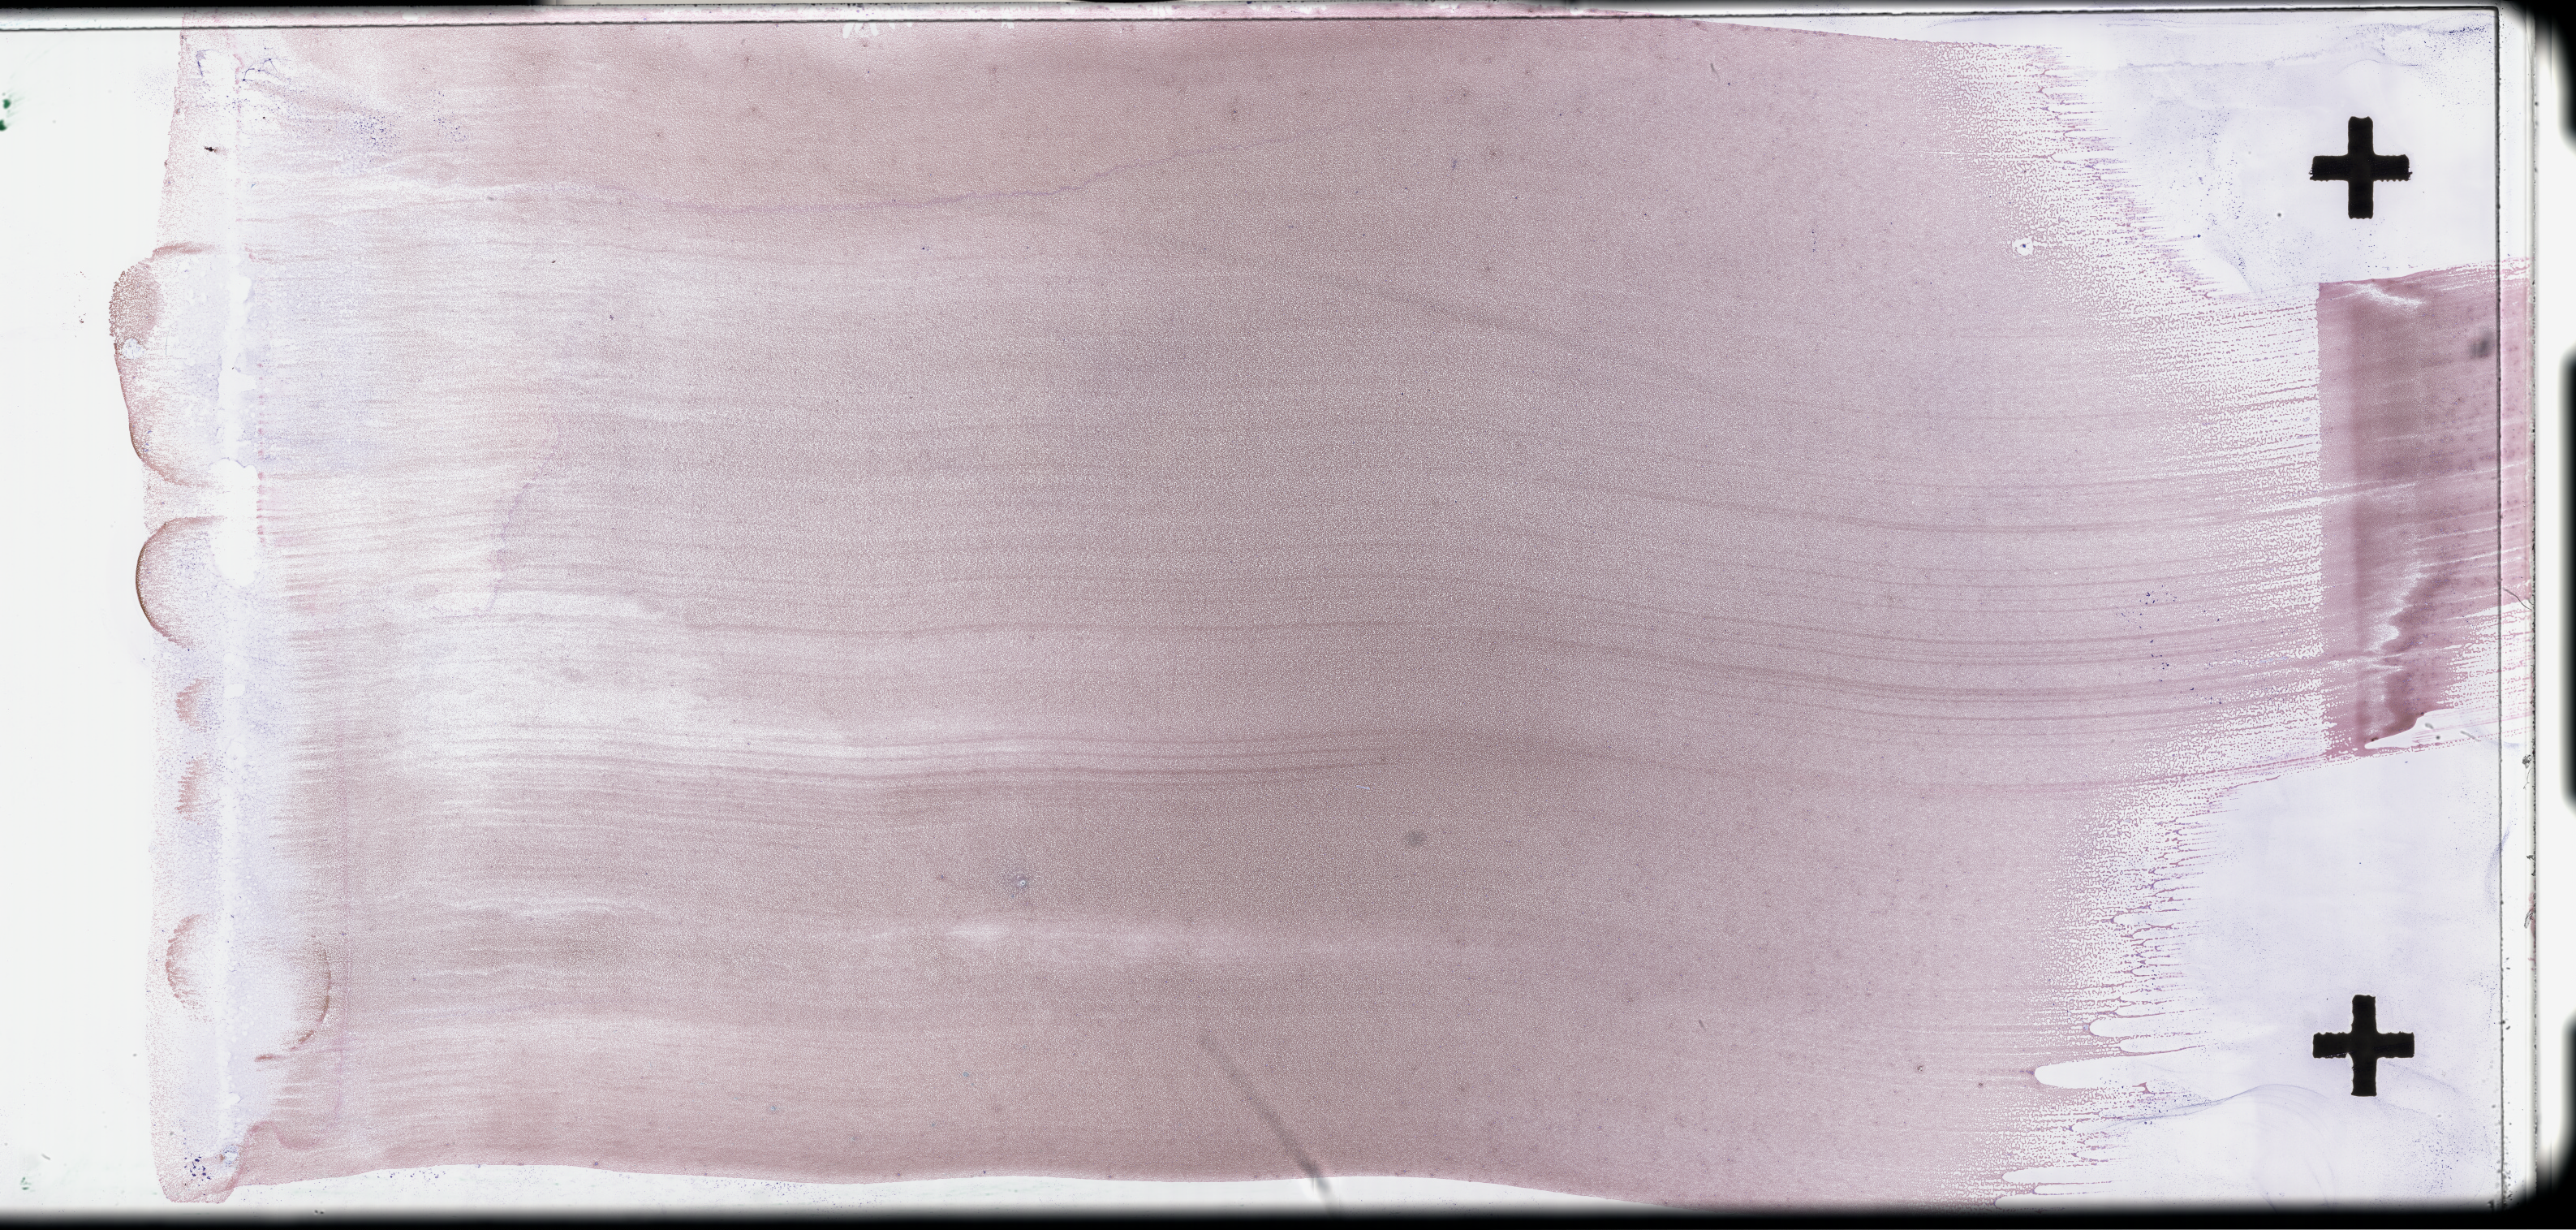
Whole-slide image of a whole blood smear, Wright-Giemsa stain — shown as a low-resolution overview of the whole scanned area (about 51.3 x 24.5 mm). Smear from an EDTA sample. Specimen time point: collected on treatment. Male patient.
From a patient with: Plasma Cell Myeloma.